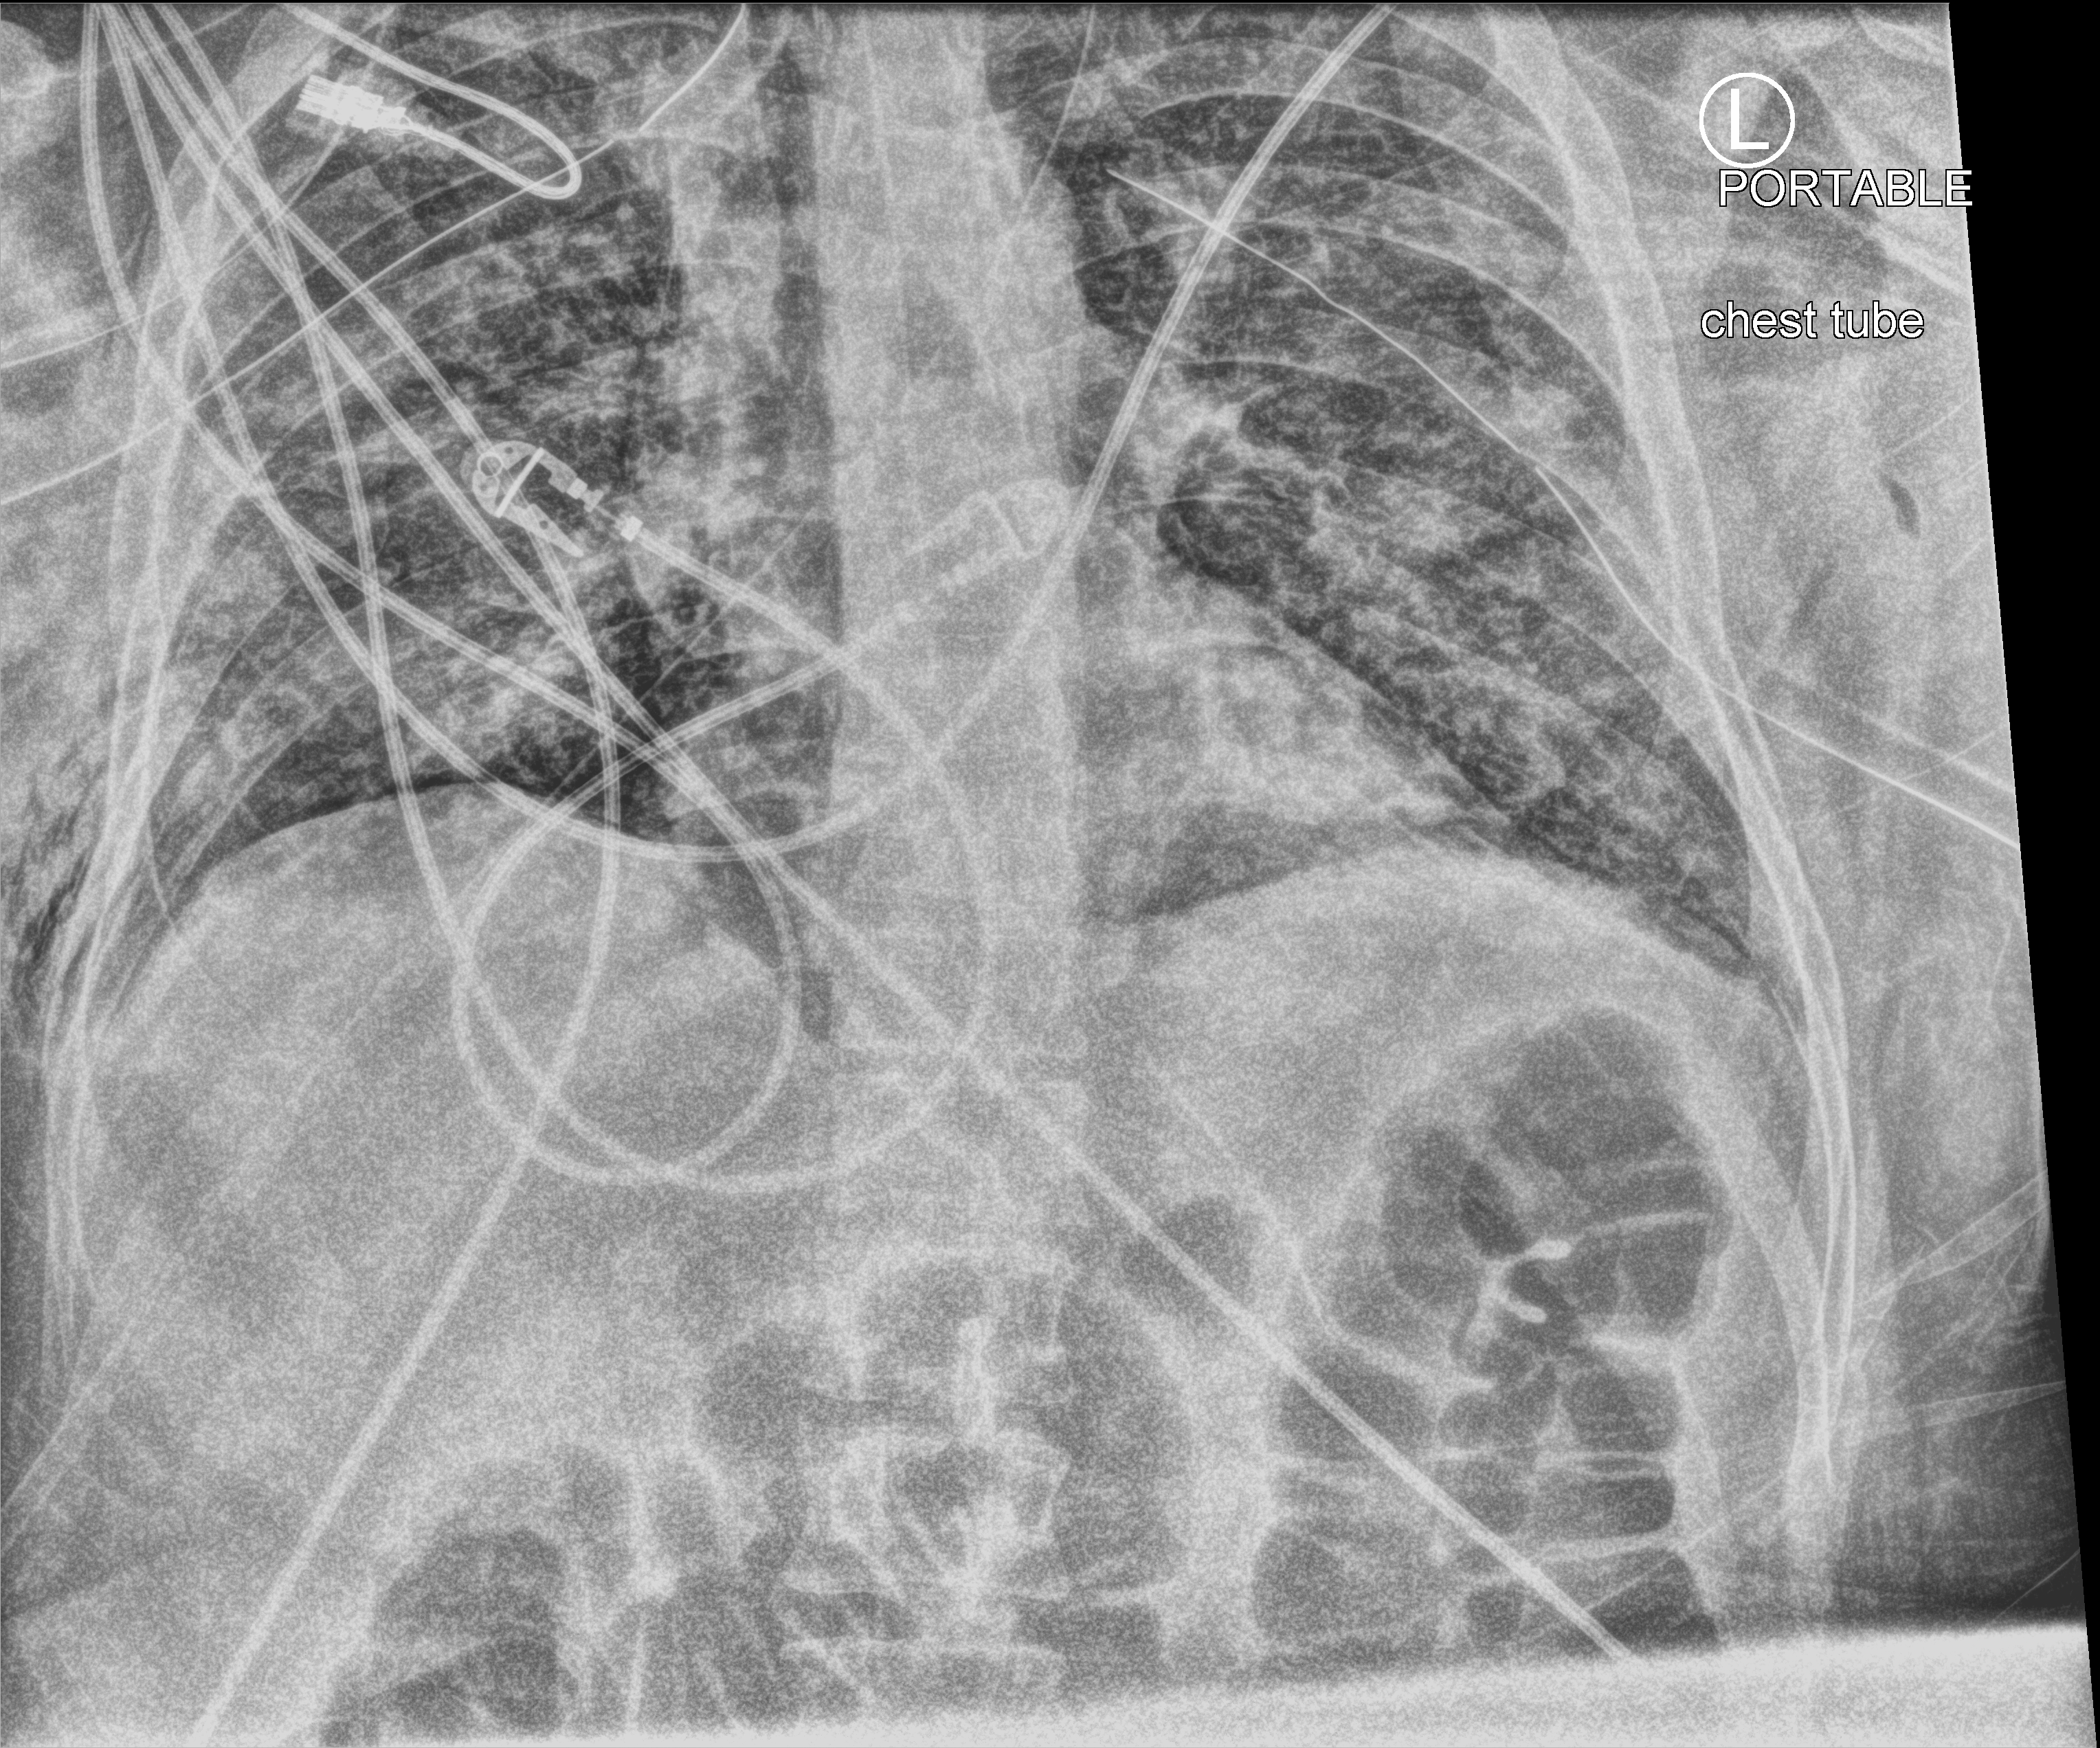
Portable chest radiograph. Patient hospitalised with COVID-19; male, aged 18–59 years.
Admission-level facts for this patient (not findings on this image; timing relative to this image not recorded): admitted to intensive care during this hospital stay: yes; hypertension (admission record): yes.